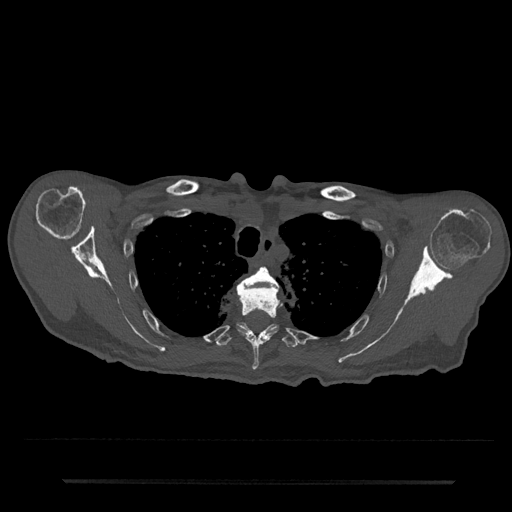
CT including the spine, one axial slice; position 613 of 797 along the scan axis; 120 kVp; bone window (W 1800 / L 400 HU); 512 × 512 image matrix. Patient: male, 74 years. Case-level facts recorded for this patient, not image findings: primary cancer: prostate.
Annotated regions visible in this slice (semi-automatically segmented with operator editing):
- T3 vertebra: box from (x=239, y=266) to (x=279, y=291) px
- T4 vertebra: (x=237, y=285)–(x=281, y=370)
- T5 vertebra: (x=215, y=322)–(x=300, y=348)